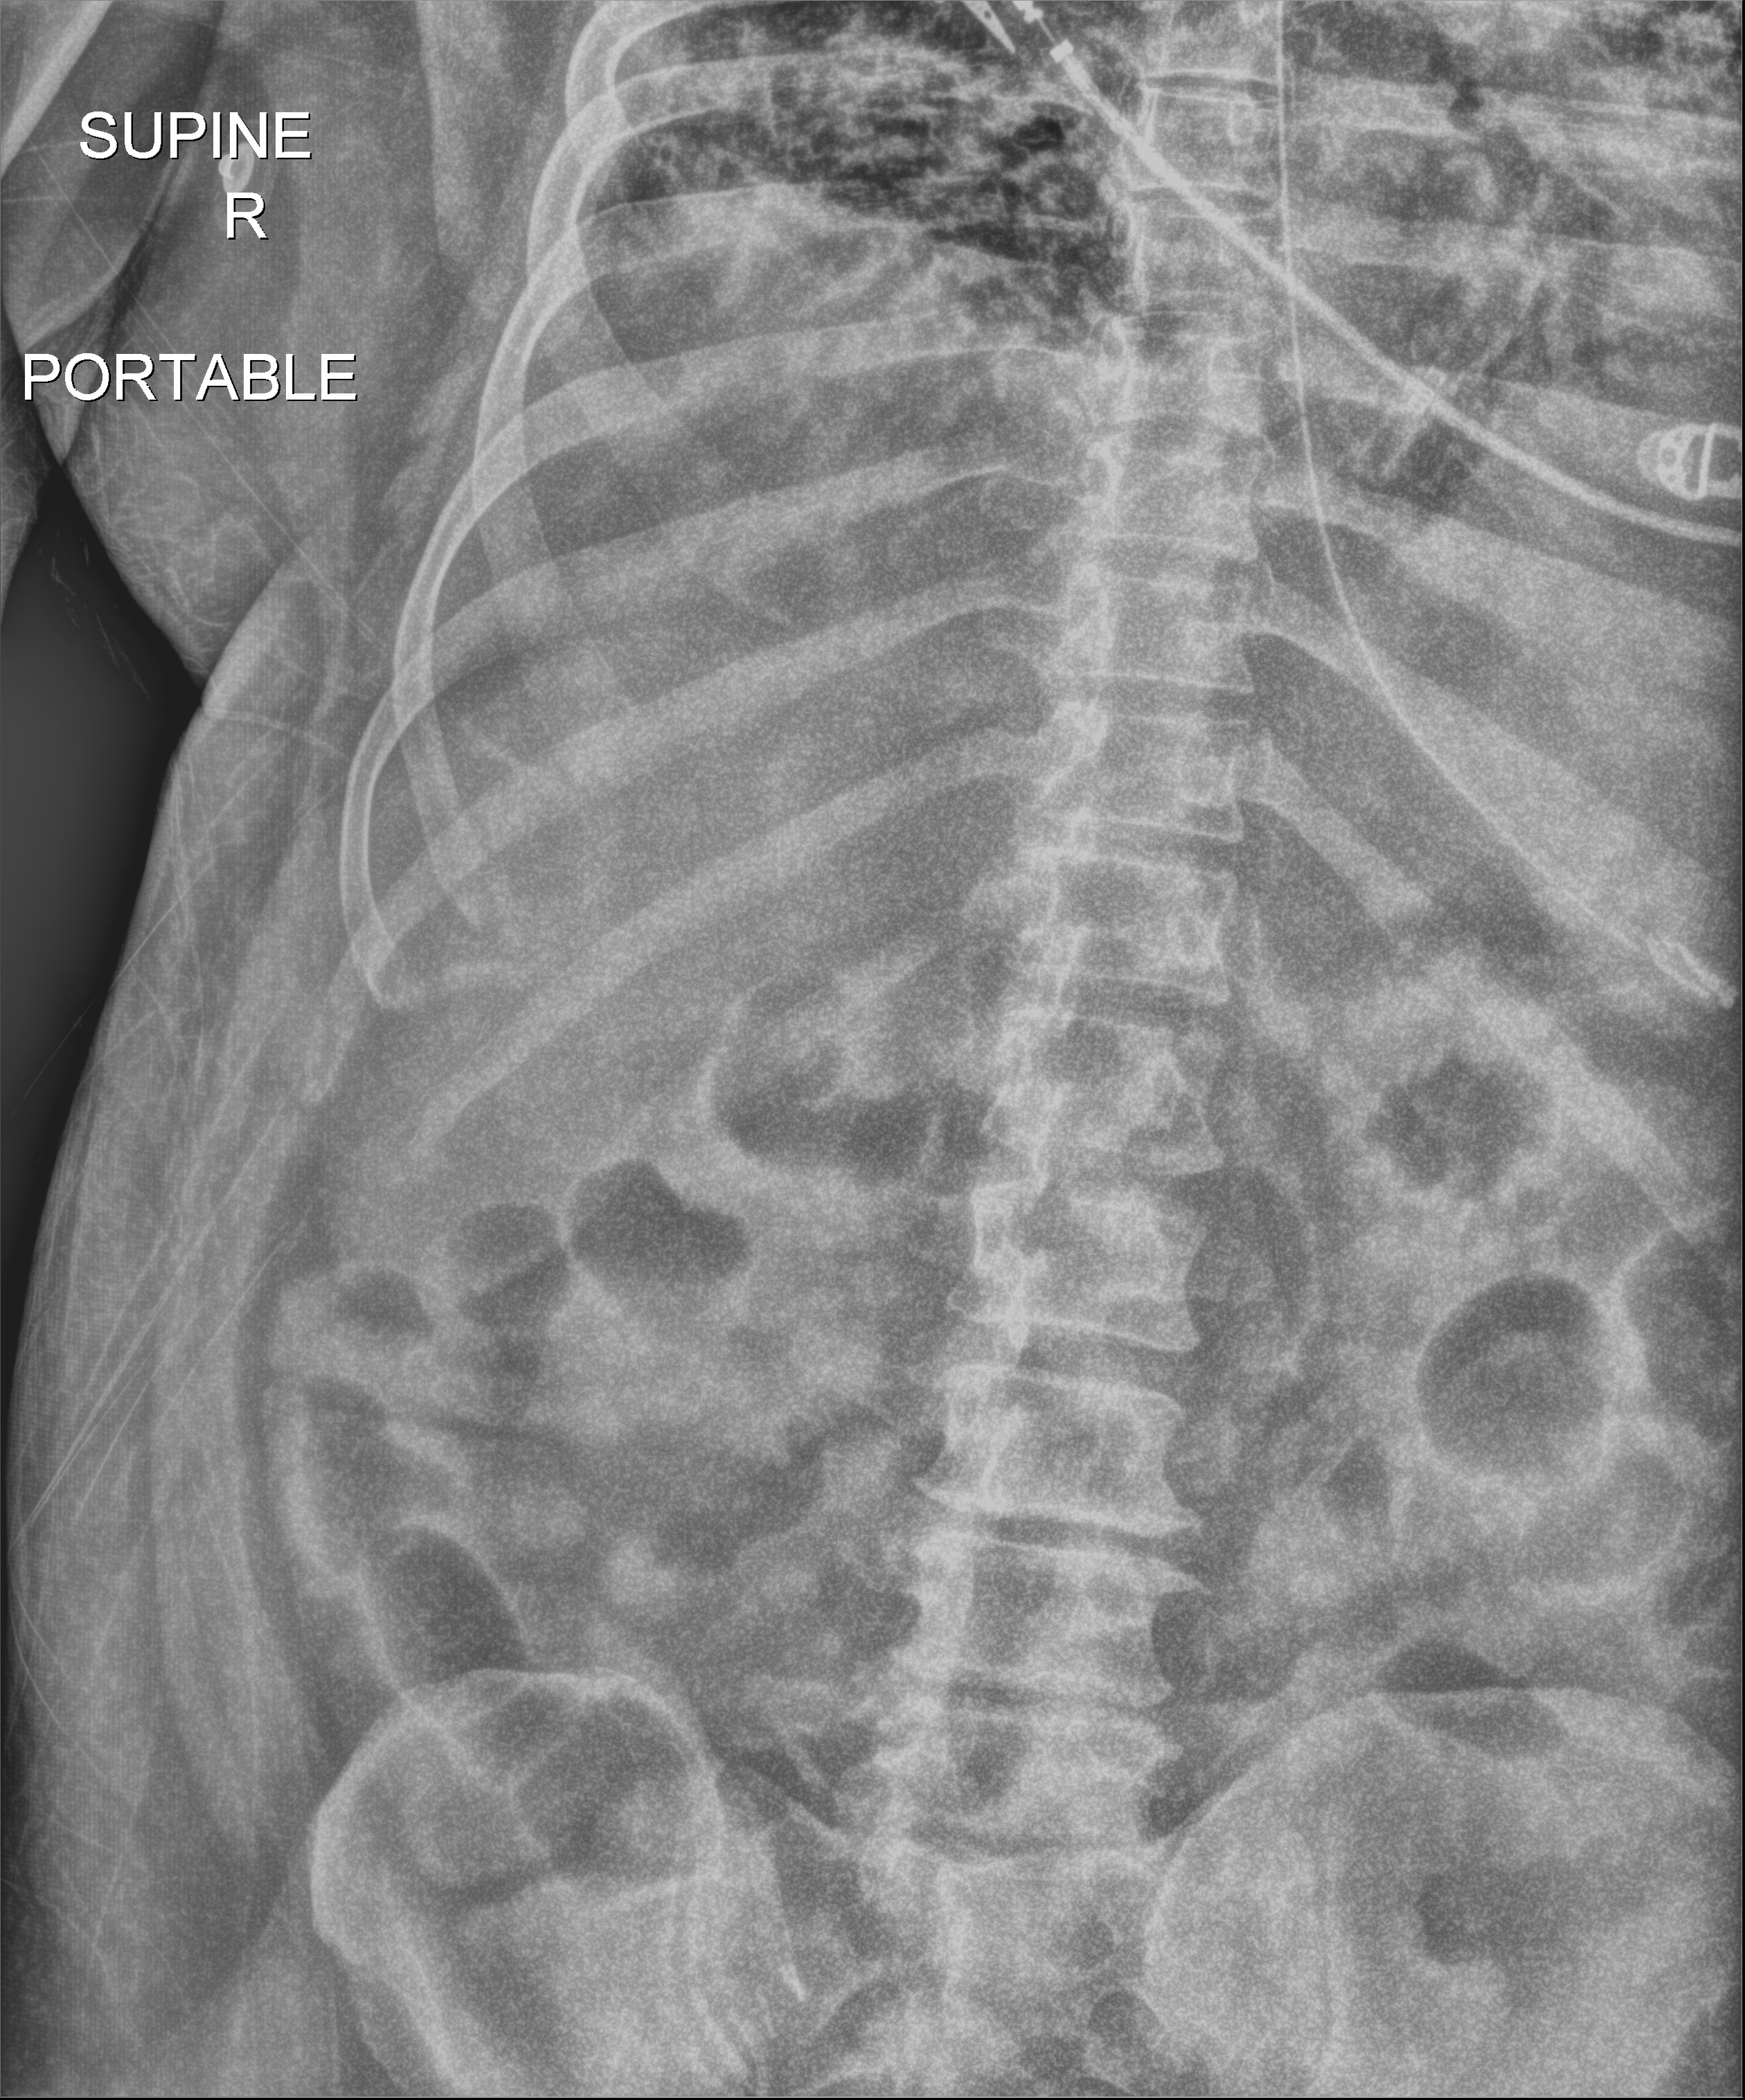
Abdomen X-ray (portable); anteroposterior (AP) projection. Patient hospitalised with COVID-19; male, aged 18–59 years.
From the hospital-stay record, not from the radiograph (when in the stay this image was taken is not recorded): admitted to intensive care during this hospital stay: yes.